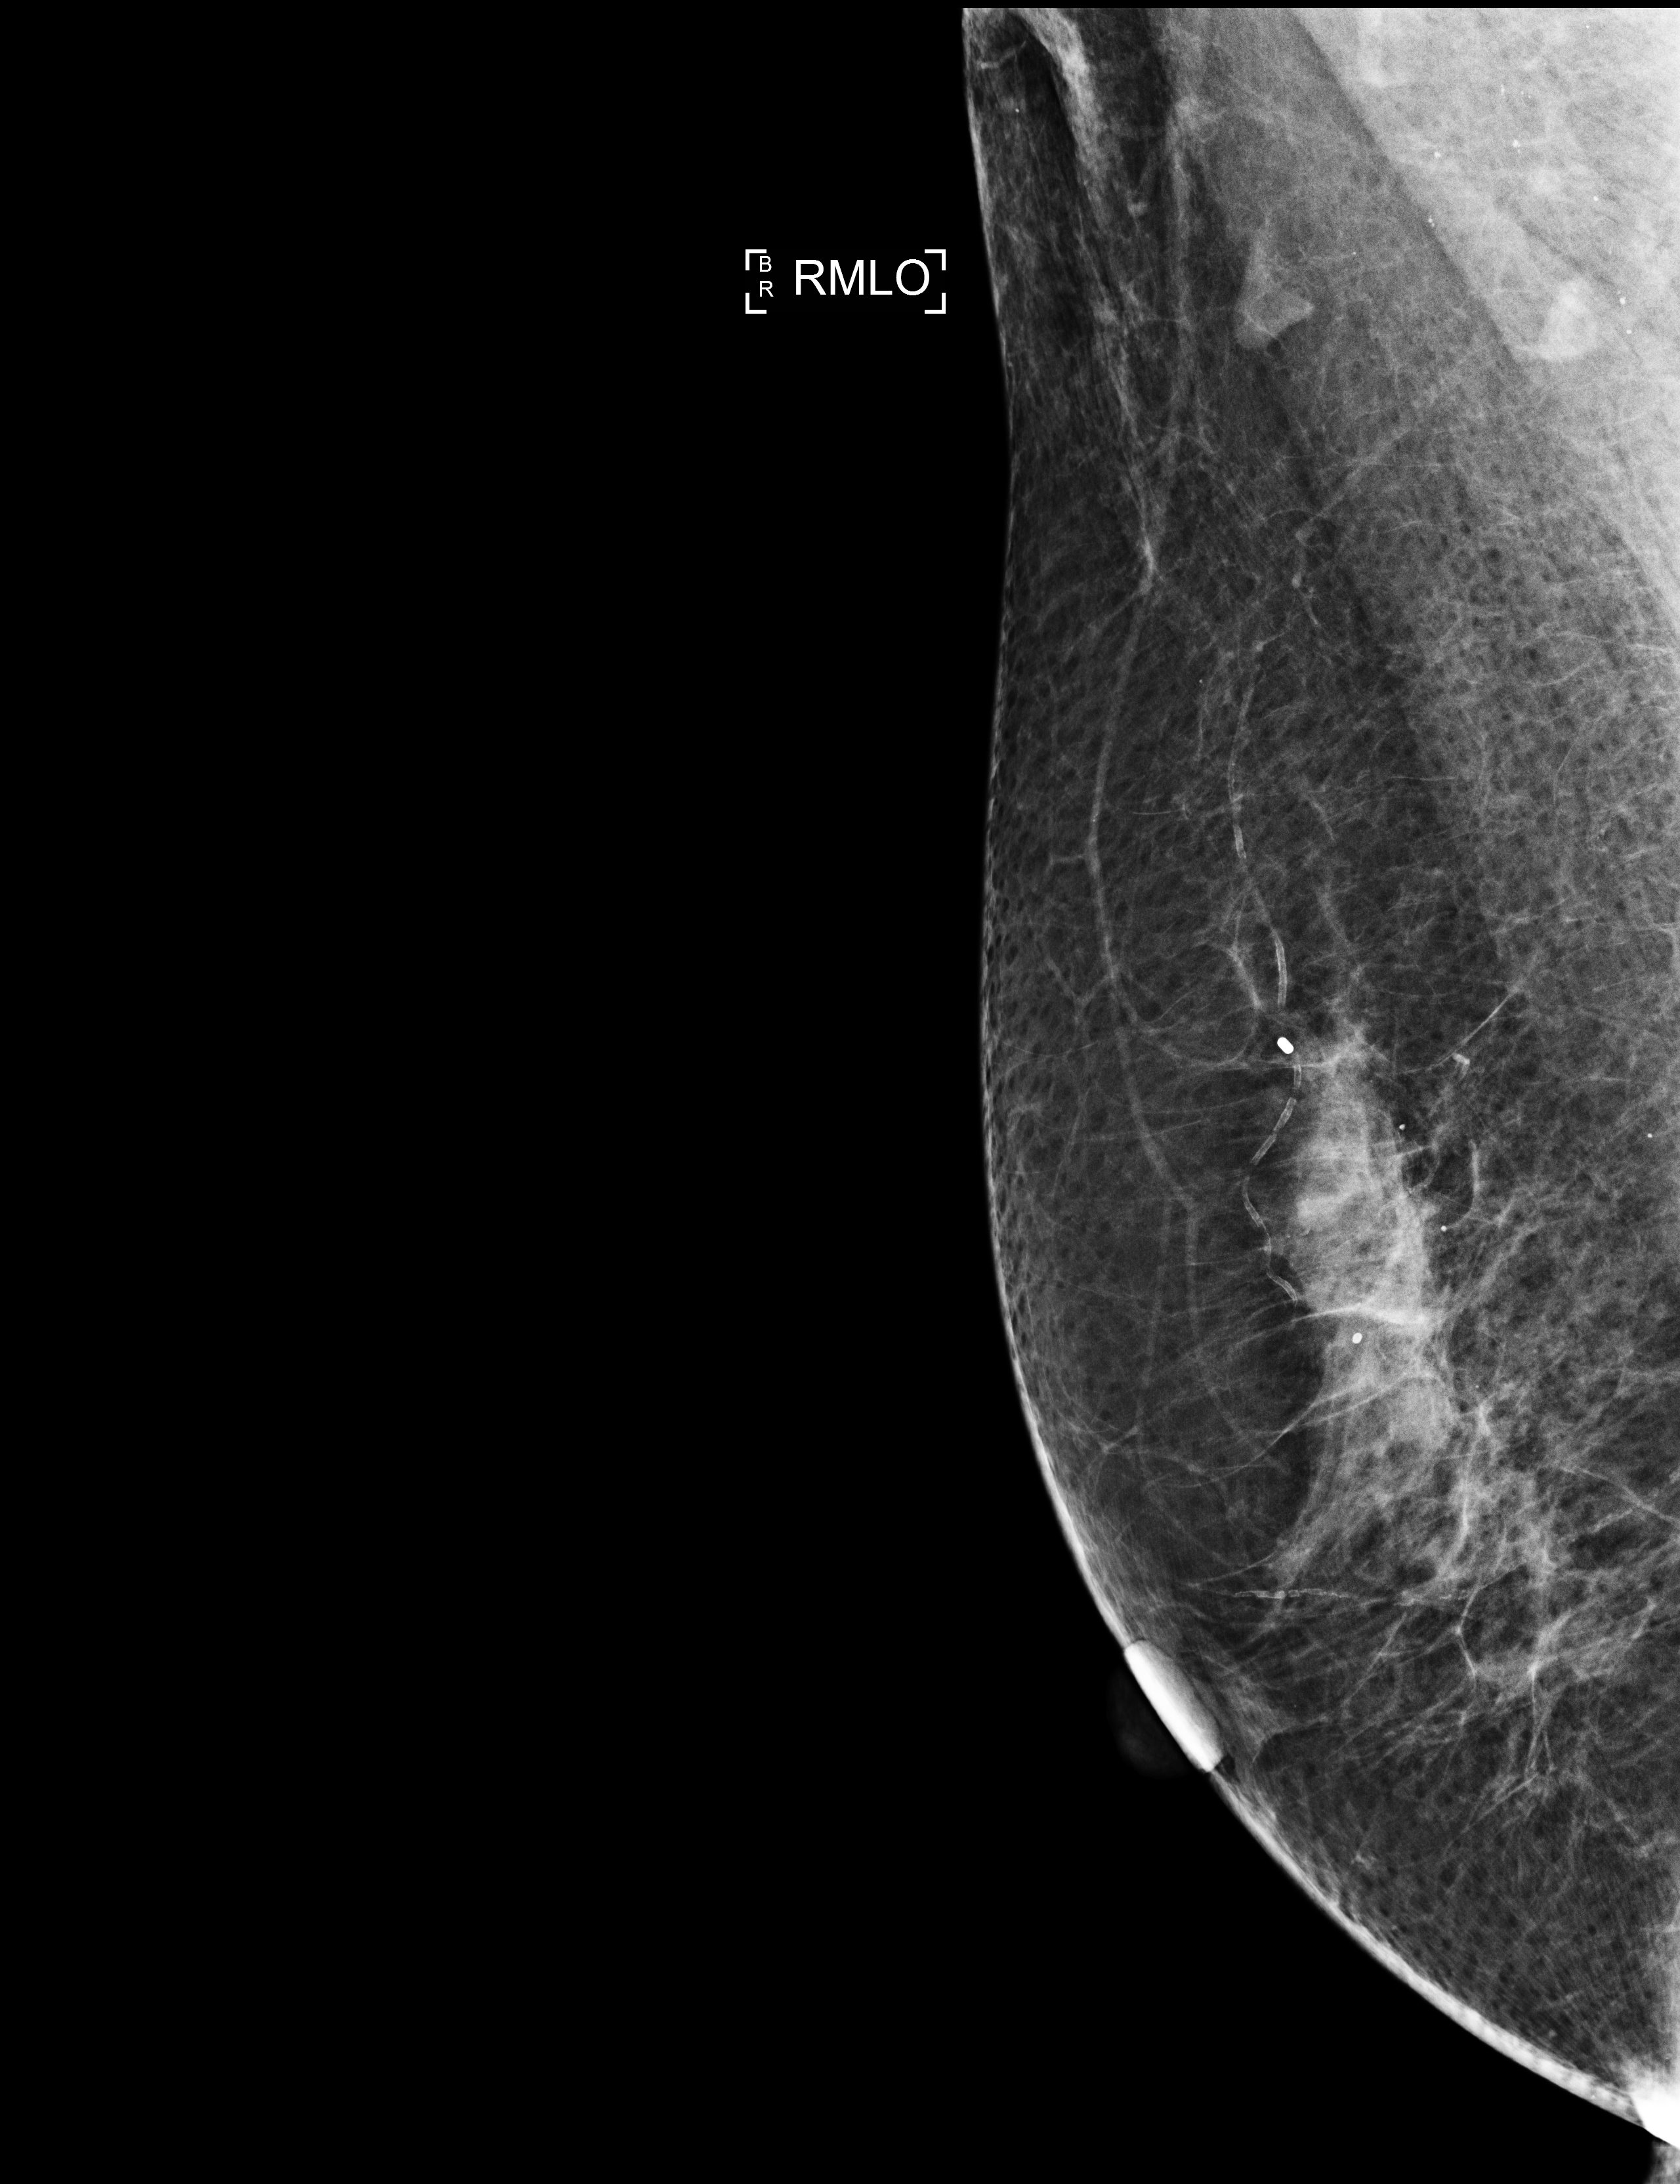
Screening examination; compressed breast thickness 65 mm. Patient aged 69 years (female).
Image type: full-field digital mammogram. Breast: right. Projection: mediolateral oblique (MLO) view.